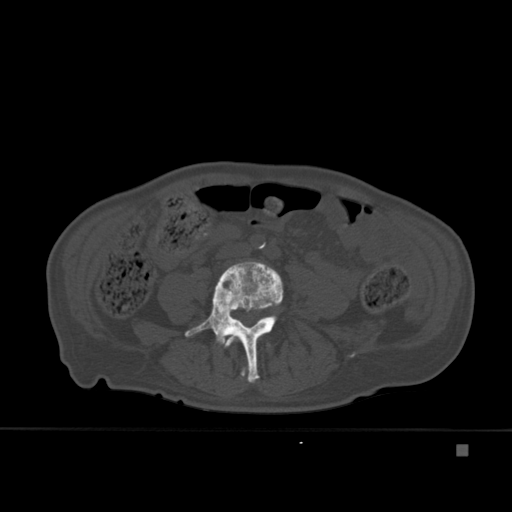
CT including the spine, one axial slice. Position 123 of 451 along the scan axis. Bone window (W 1800 / L 400 HU). 1.5 mm slice thickness. 512 × 512 image matrix, field of view 378 × 378 mm. Male patient, age 75 years. From the clinical record (not read from this slice): primary cancer: prostate.
Annotated regions visible in this slice (semi-automatic segmentation, software-assisted and operator-edited):
- L3 vertebra: bounding box <224,334,270,377> (left, top, right, bottom; pixels)
- L4 vertebra: <185,262,284,383>